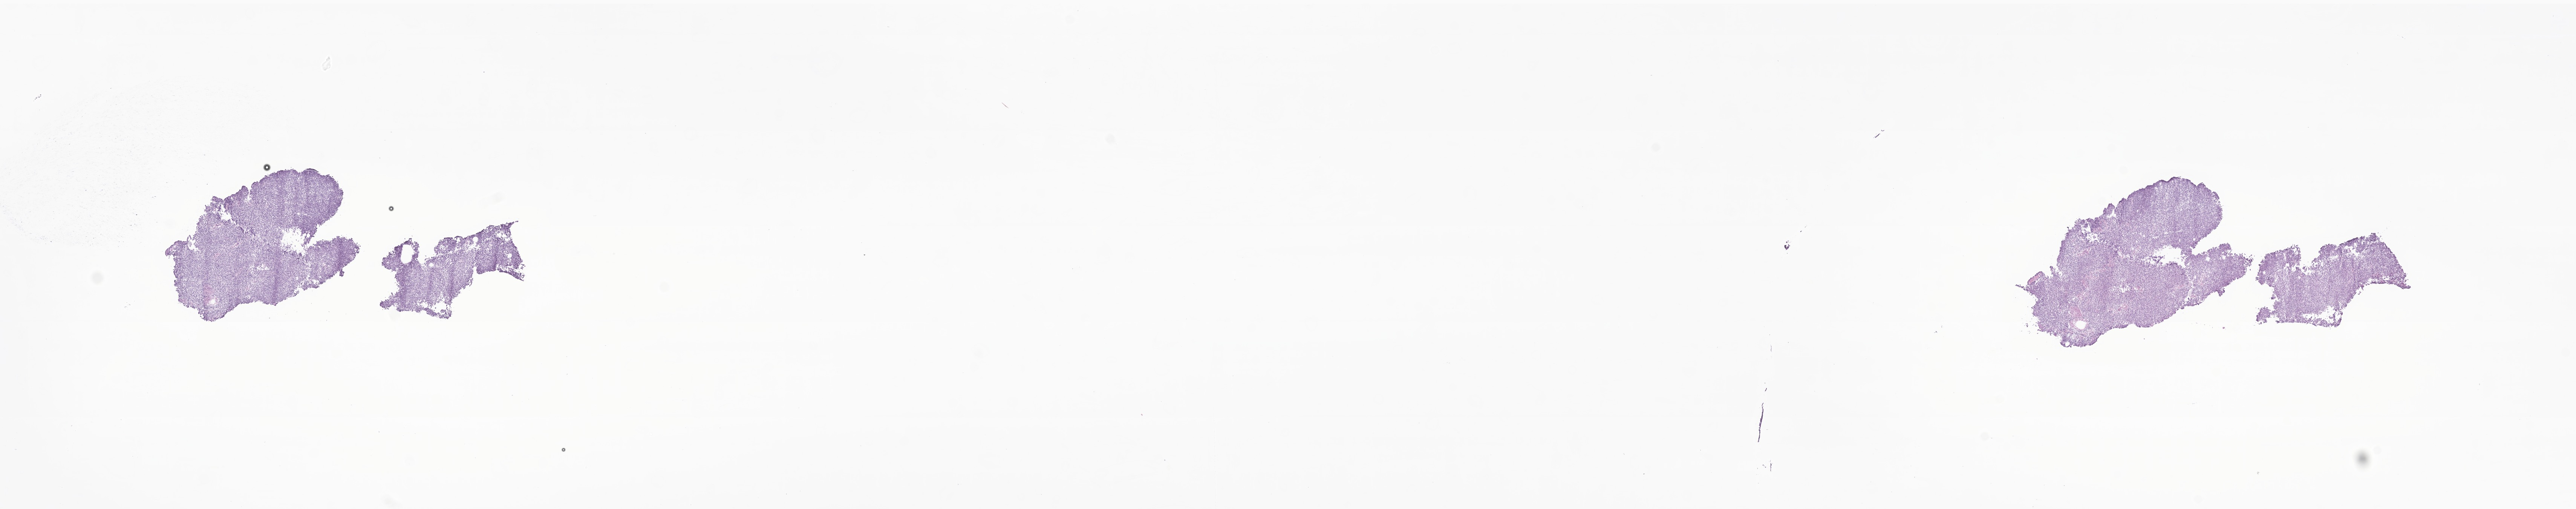
H&E whole-slide image of tumor tissue from the brain — whole scanned area (about 28.8 x 5.7 mm) shown as a low-resolution overview, frozen section. Patient female; age 143 months (11 years 11 months).
- diagnosis (ICD-O-3 morphology term): Medulloblastoma, NOS